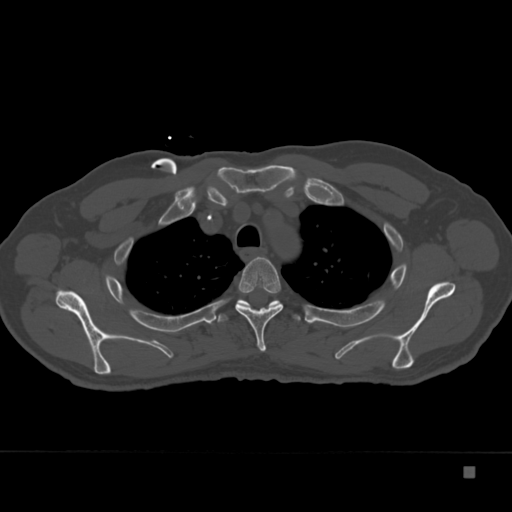
CT including the spine, one axial slice; slice 283 of 332 in the series (ordered by position); bone window (W 1800 / L 400 HU); 1.5 mm slice thickness; 512 × 512 image matrix, field of view 389 × 389 mm. Male patient, age 72 years. From the clinical record (not read from this slice): primary cancer: skeletal.
Annotated regions visible in this slice (semi-automatically segmented with operator editing):
- T3 vertebra: bounding box (x1, y1, x2, y2) in pixels: (235, 257, 283, 352)
- T4 vertebra: (216, 299, 301, 323)